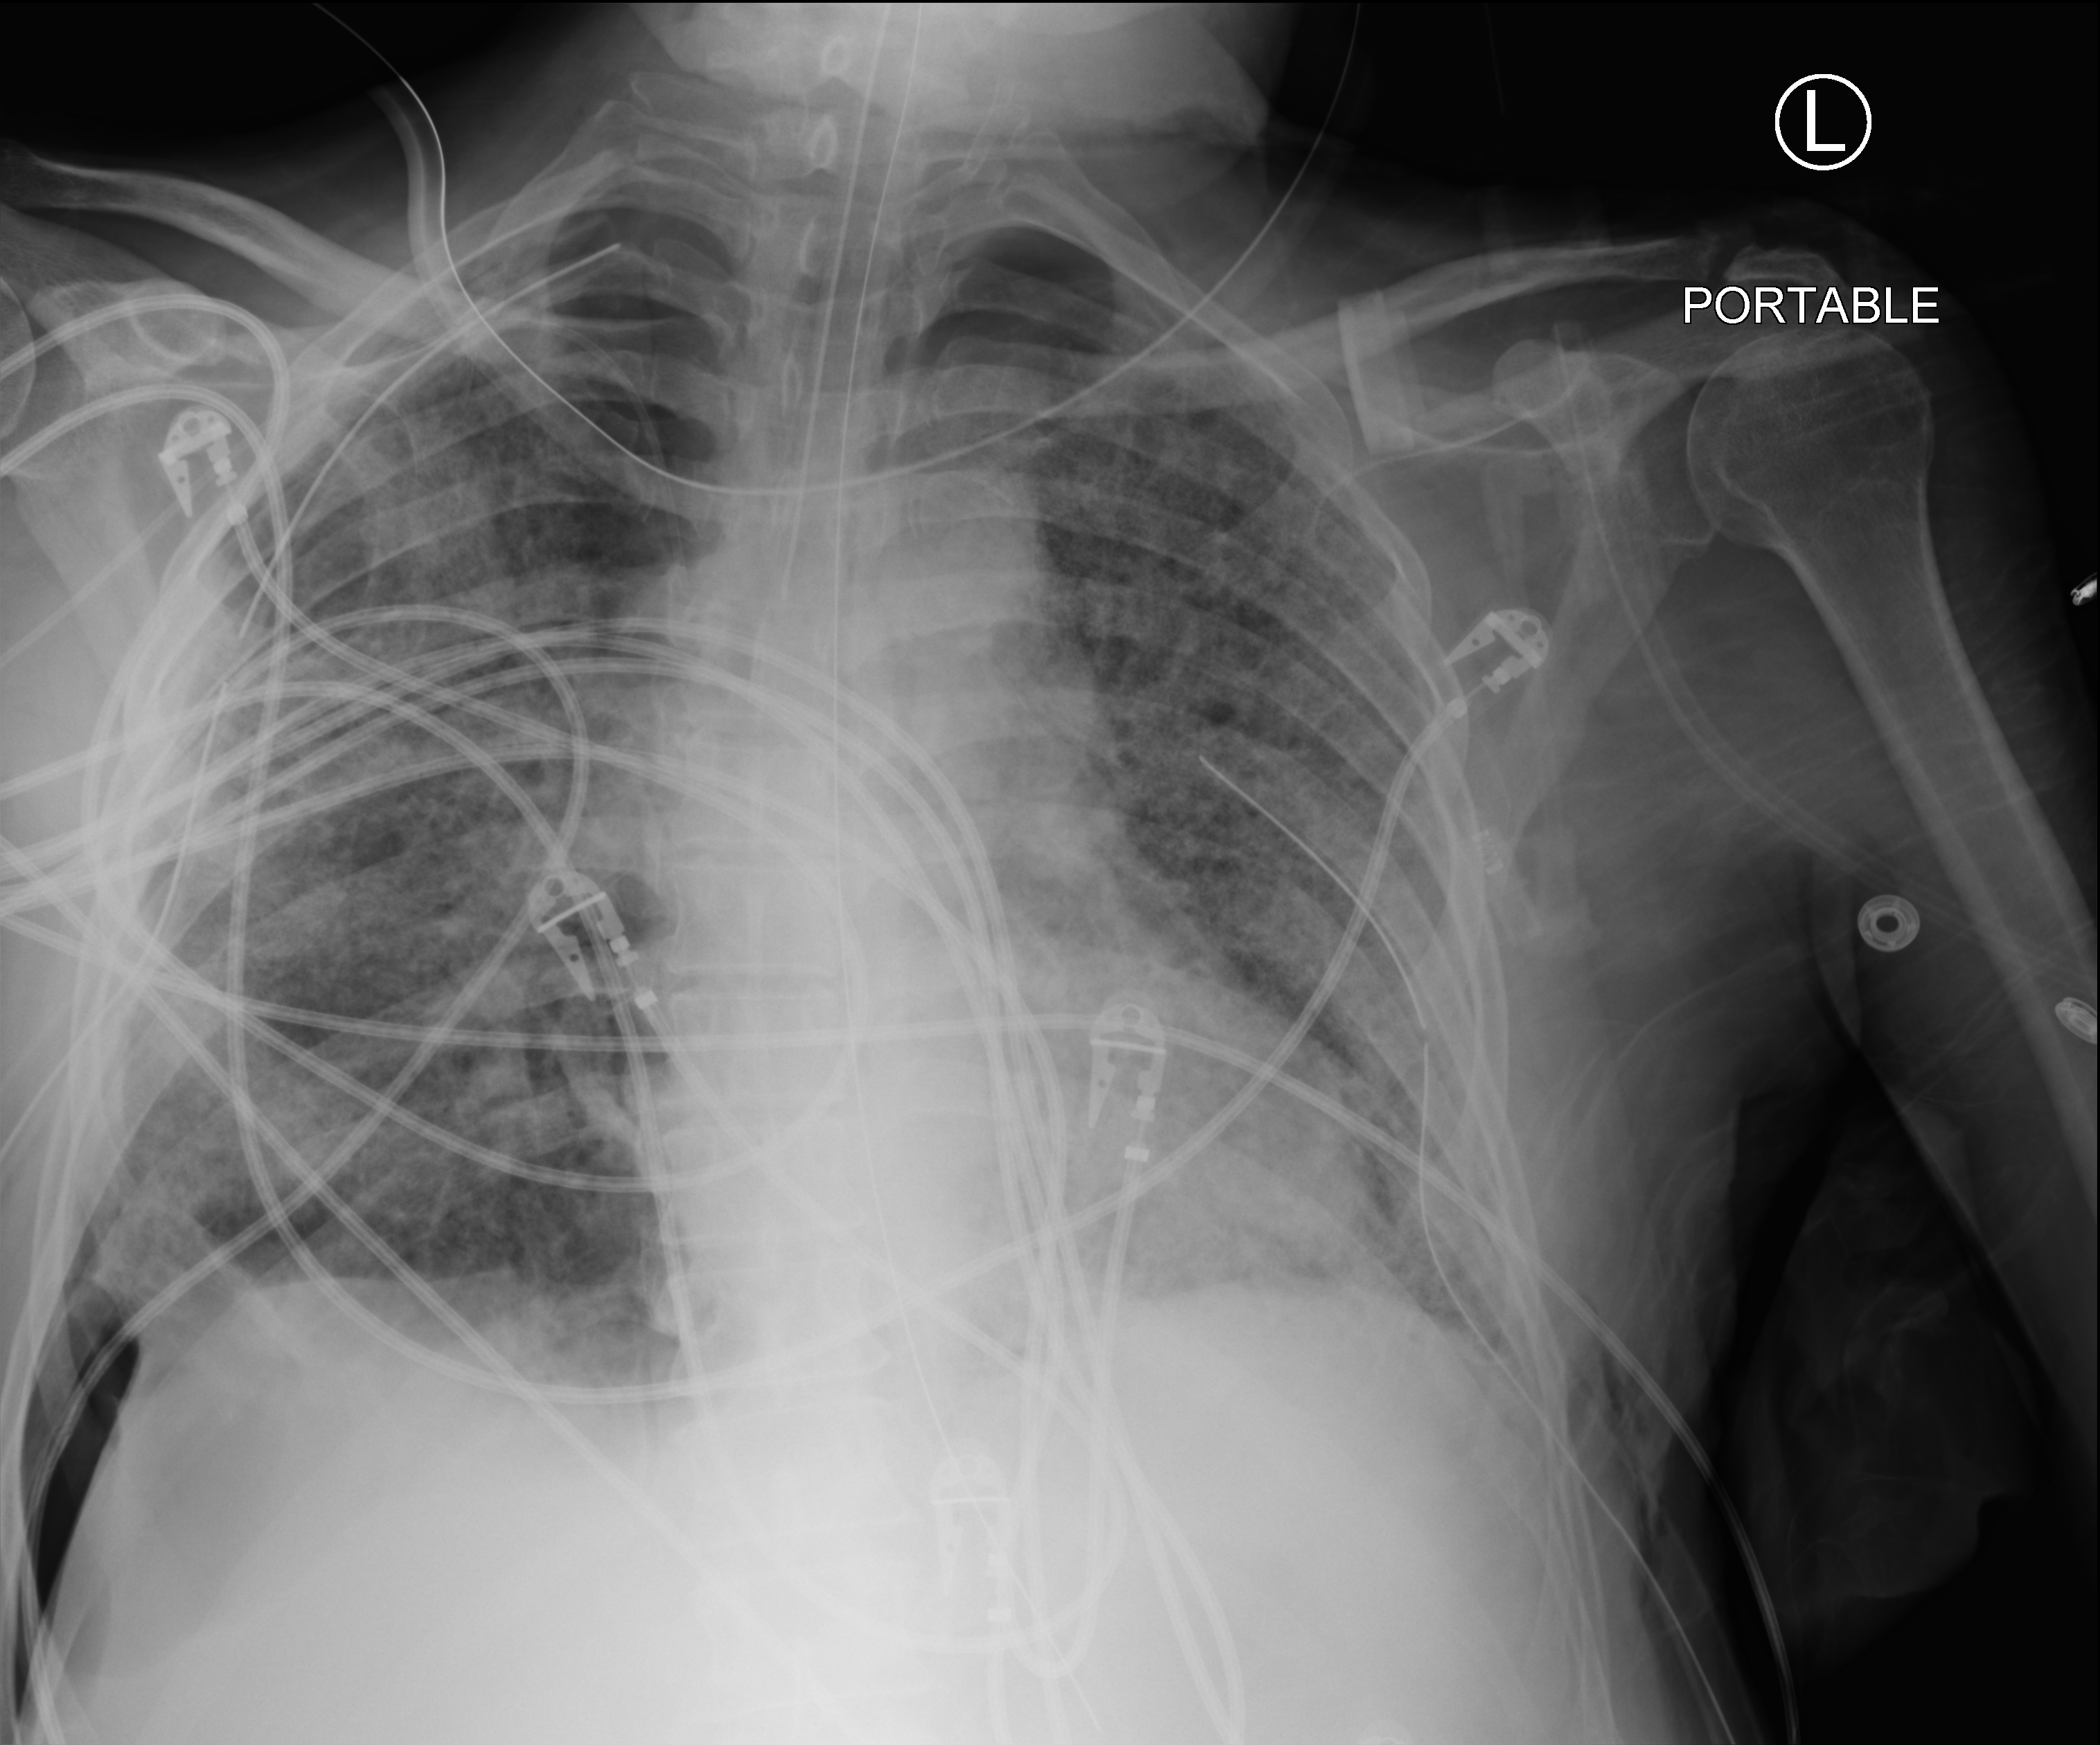
Chest X-ray (portable), anteroposterior (AP) projection. Male patient hospitalised with COVID-19, age 60–74 years.
Hospital-stay facts (about this admission, not read from this image; timing relative to this image not recorded): smoking status (admission record): never; mechanically ventilated during this hospital stay: yes; admitted to intensive care during this hospital stay: yes.